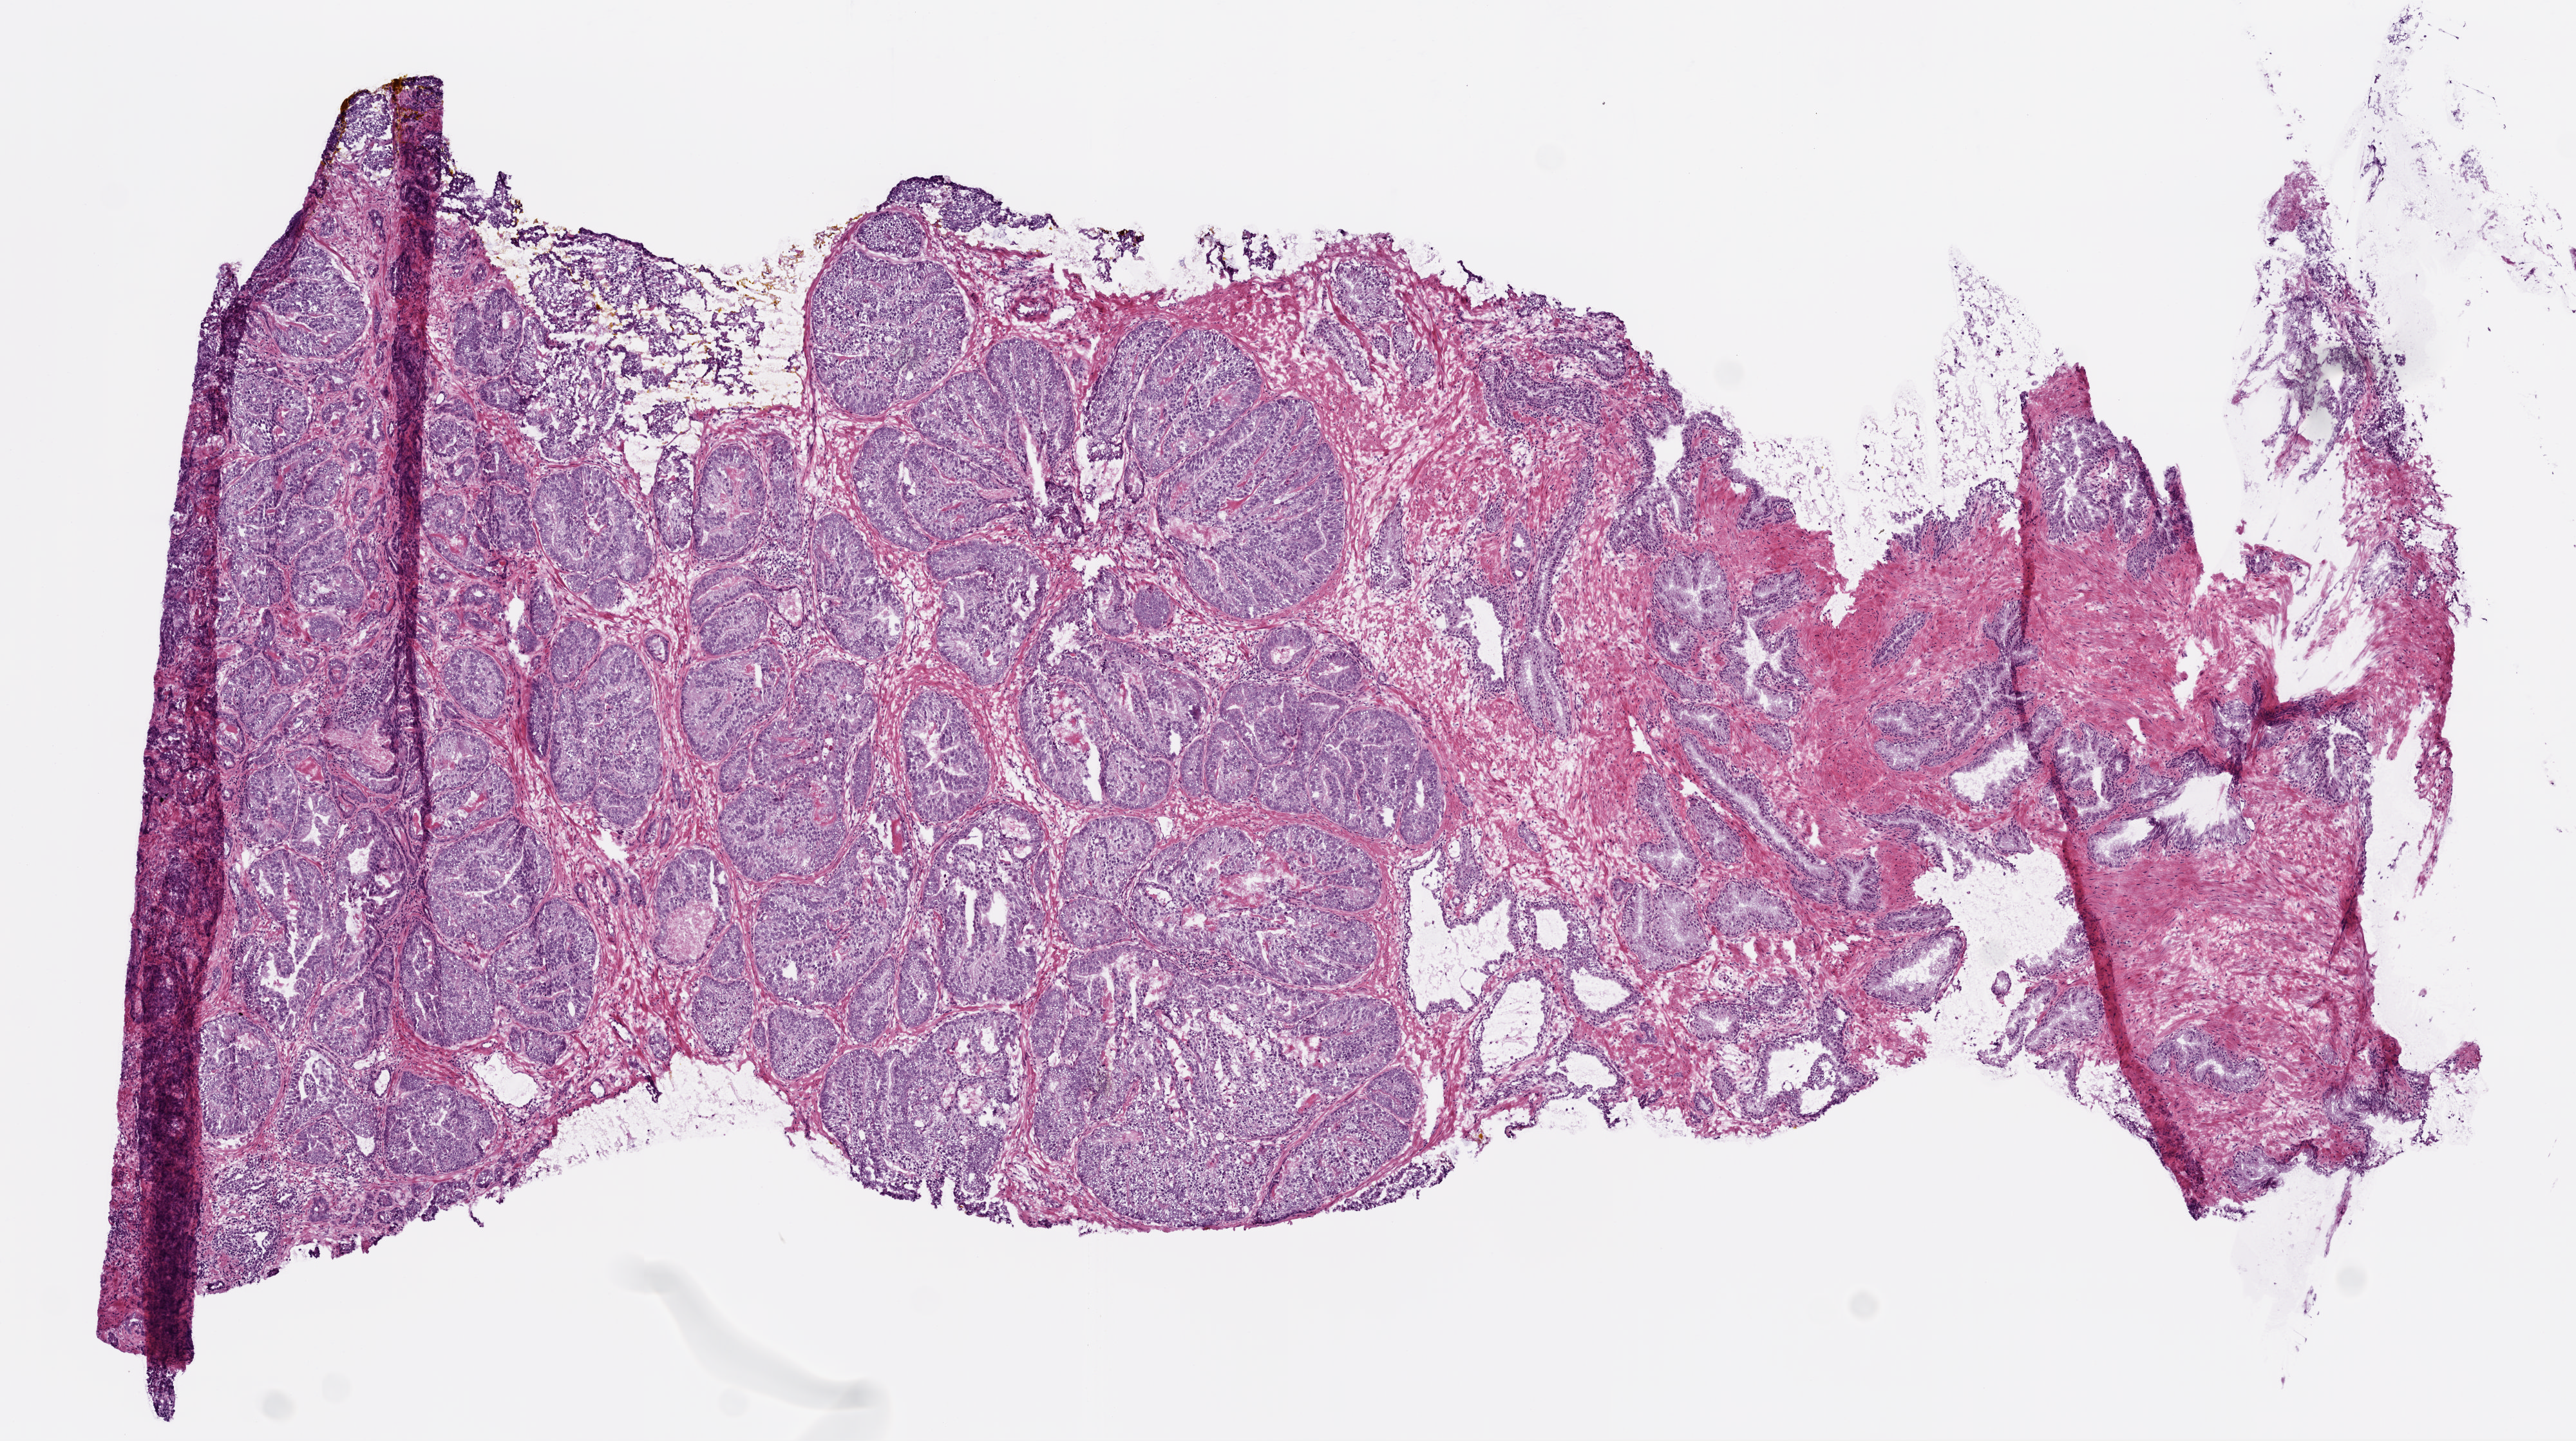
Digitized H&E-stained tissue section (whole slide) — whole scanned area (about 8.0 x 4.5 mm) shown as a low-resolution overview, frozen section, primary tumour sample from the prostate. Patient: male, age at initial diagnosis 61 years. Gleason score: 7 (3+4). Composition of this section per pathologist review: tumour cells 65%, tumour nuclei 70%, normal cells 20%, stromal cells 15%, necrosis 0%. Infiltration values recorded for this section: lymphocyte infiltration 0%, monocyte infiltration 0%, neutrophil infiltration 0%.
- pathologic diagnosis: Acinar cell carcinoma (prostate gland)
- laterality: bilateral